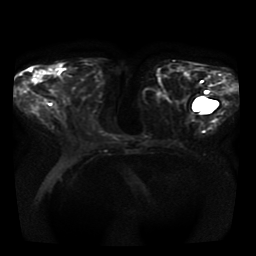
Breast MRI, one axial slice; slice 15 of 41 in the series (ordered by position); diffusion-weighted series; image 2 of 4 stored at this slice position (different b-values; order by instance number); 1.5 T; 5 mm slice thickness; 256 × 256 image matrix, field of view 350 × 350 mm. Female patient.
Outlined on this slice (manually delineated by an expert):
- tumour on diffusion-weighted imaging: bounding box (x1, y1, x2, y2) in pixels: (29, 72, 44, 84)